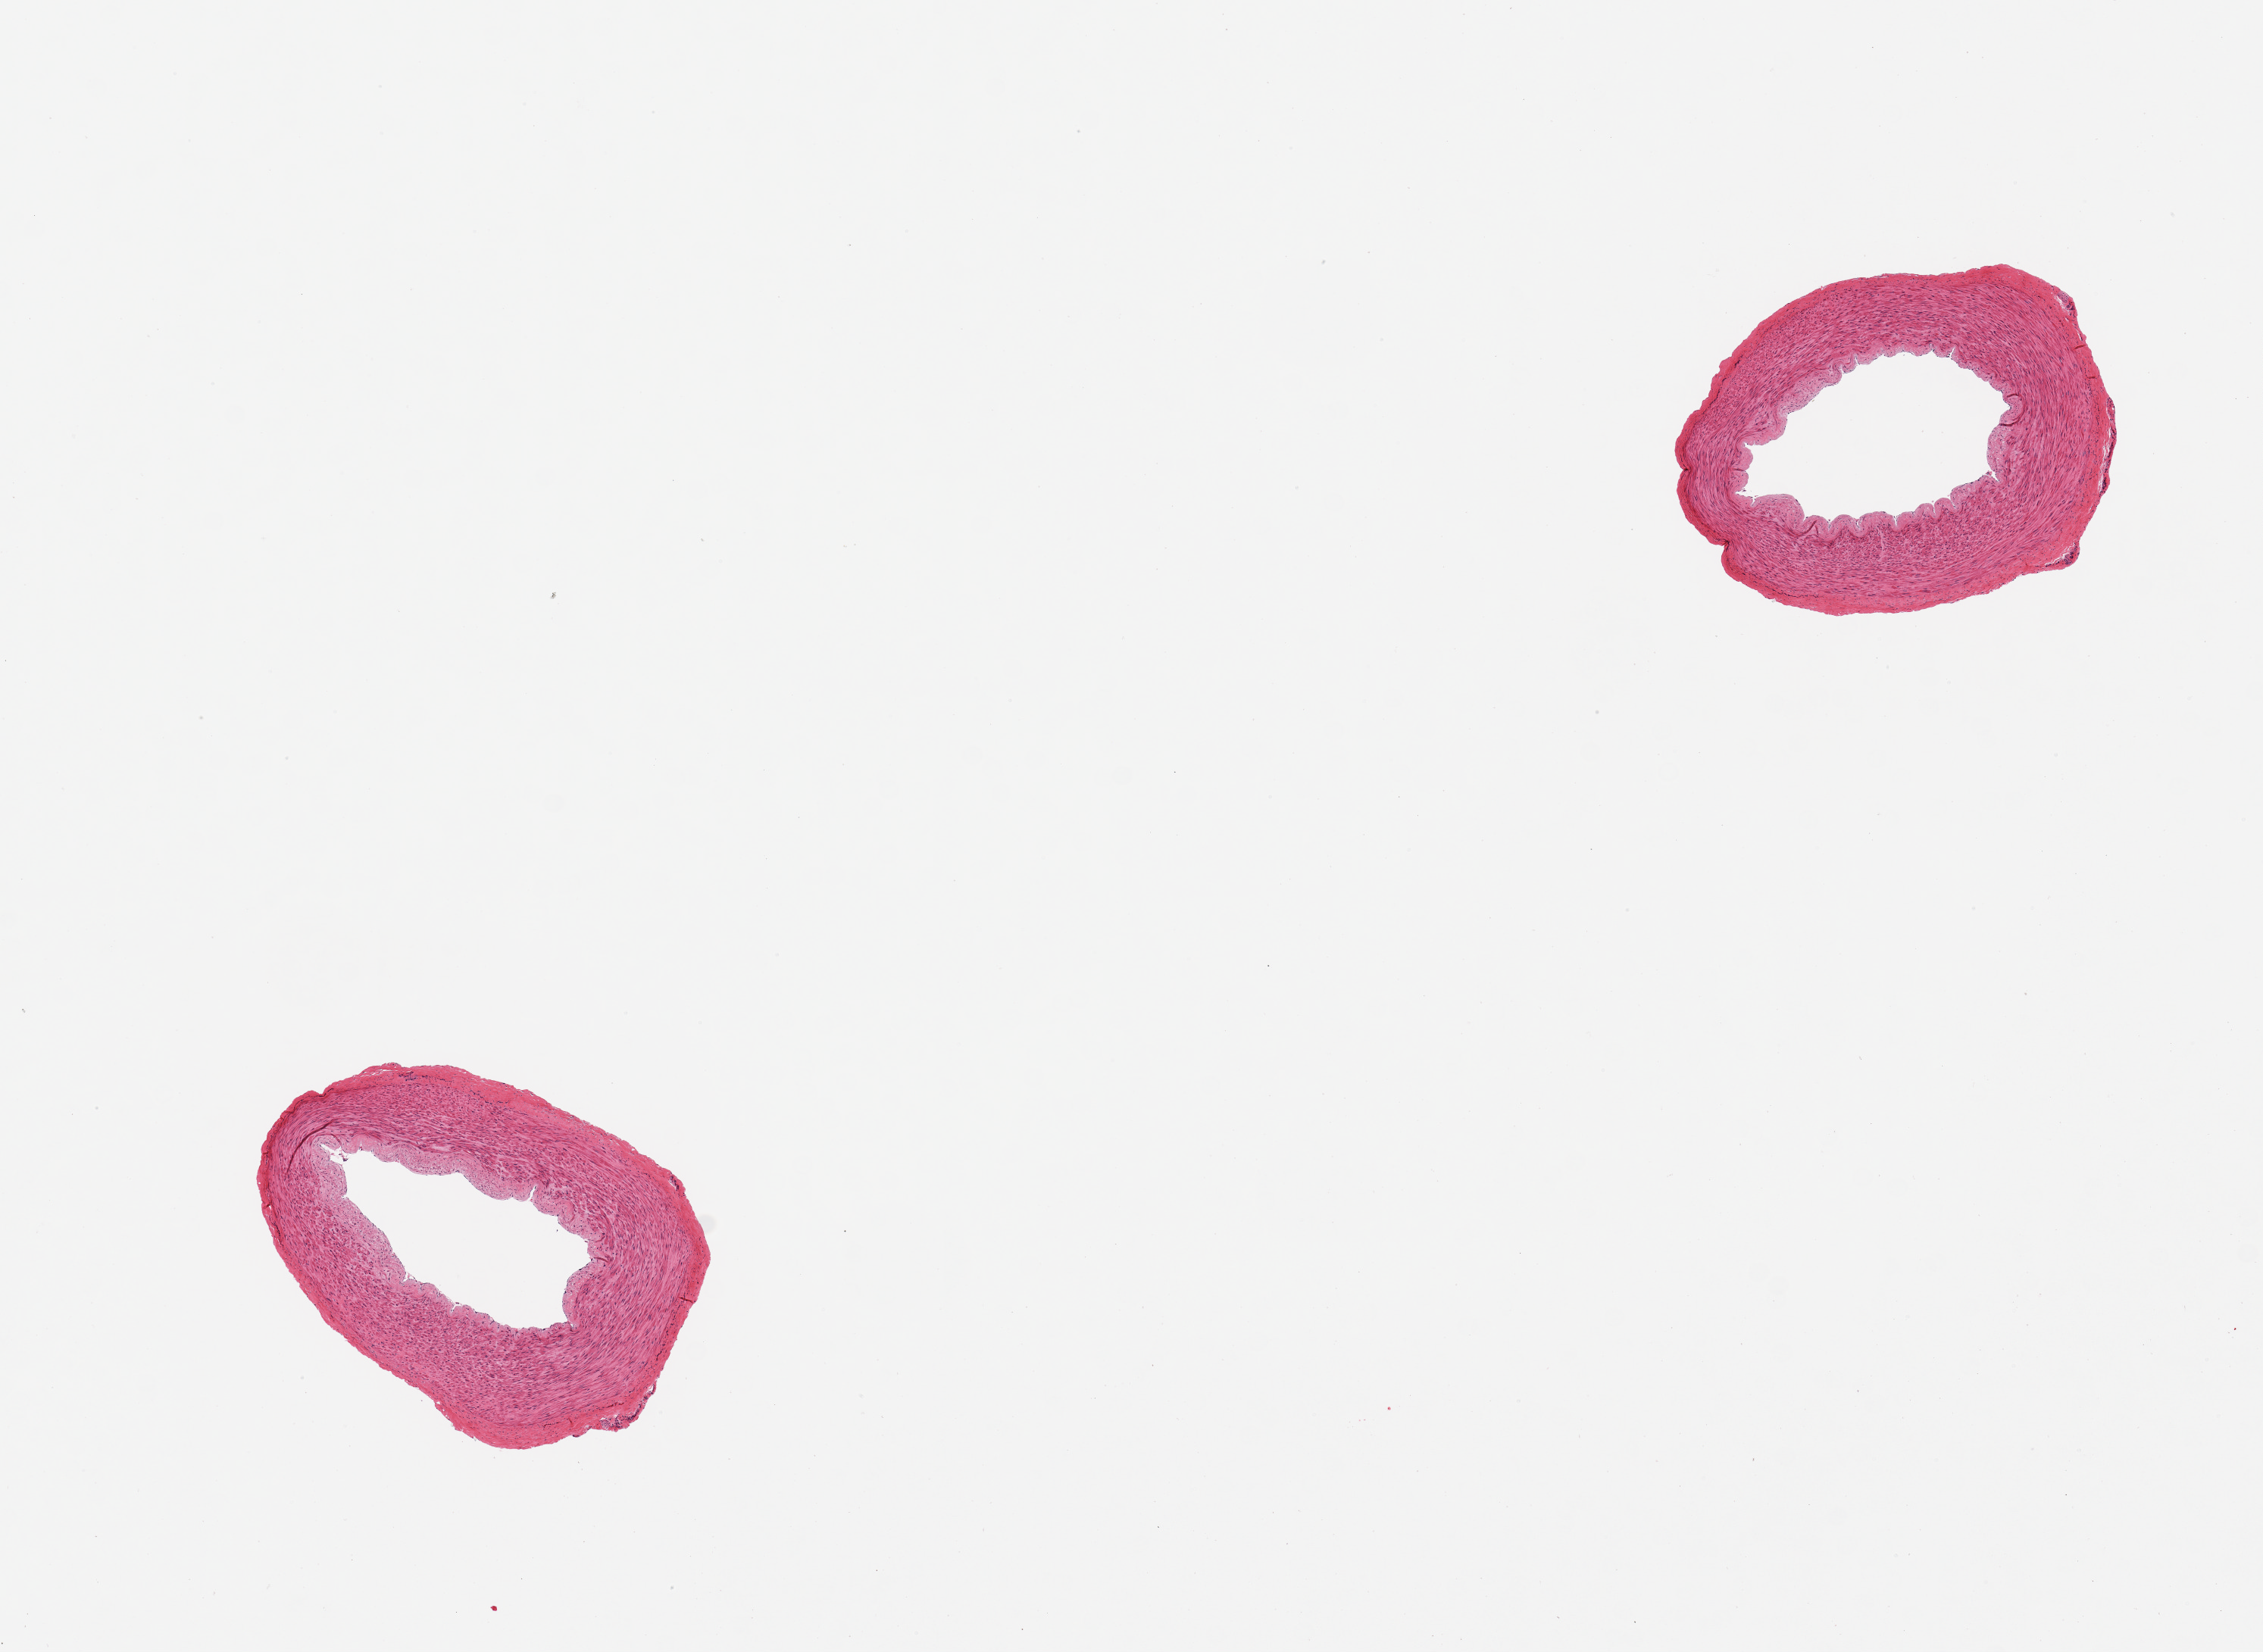
Digitized hematoxylin and eosin (H&E)-stained section — a low-resolution overview of the entire scanned area, about 11.8 x 8.6 mm (from a 20x scan); PAXgene-fixed, paraffin-embedded tissue; target tissue: tibial artery; tissue donor sample. Donor: male.
Reviewer comment on this tissue sample: 2 pieces. Well trimmed.